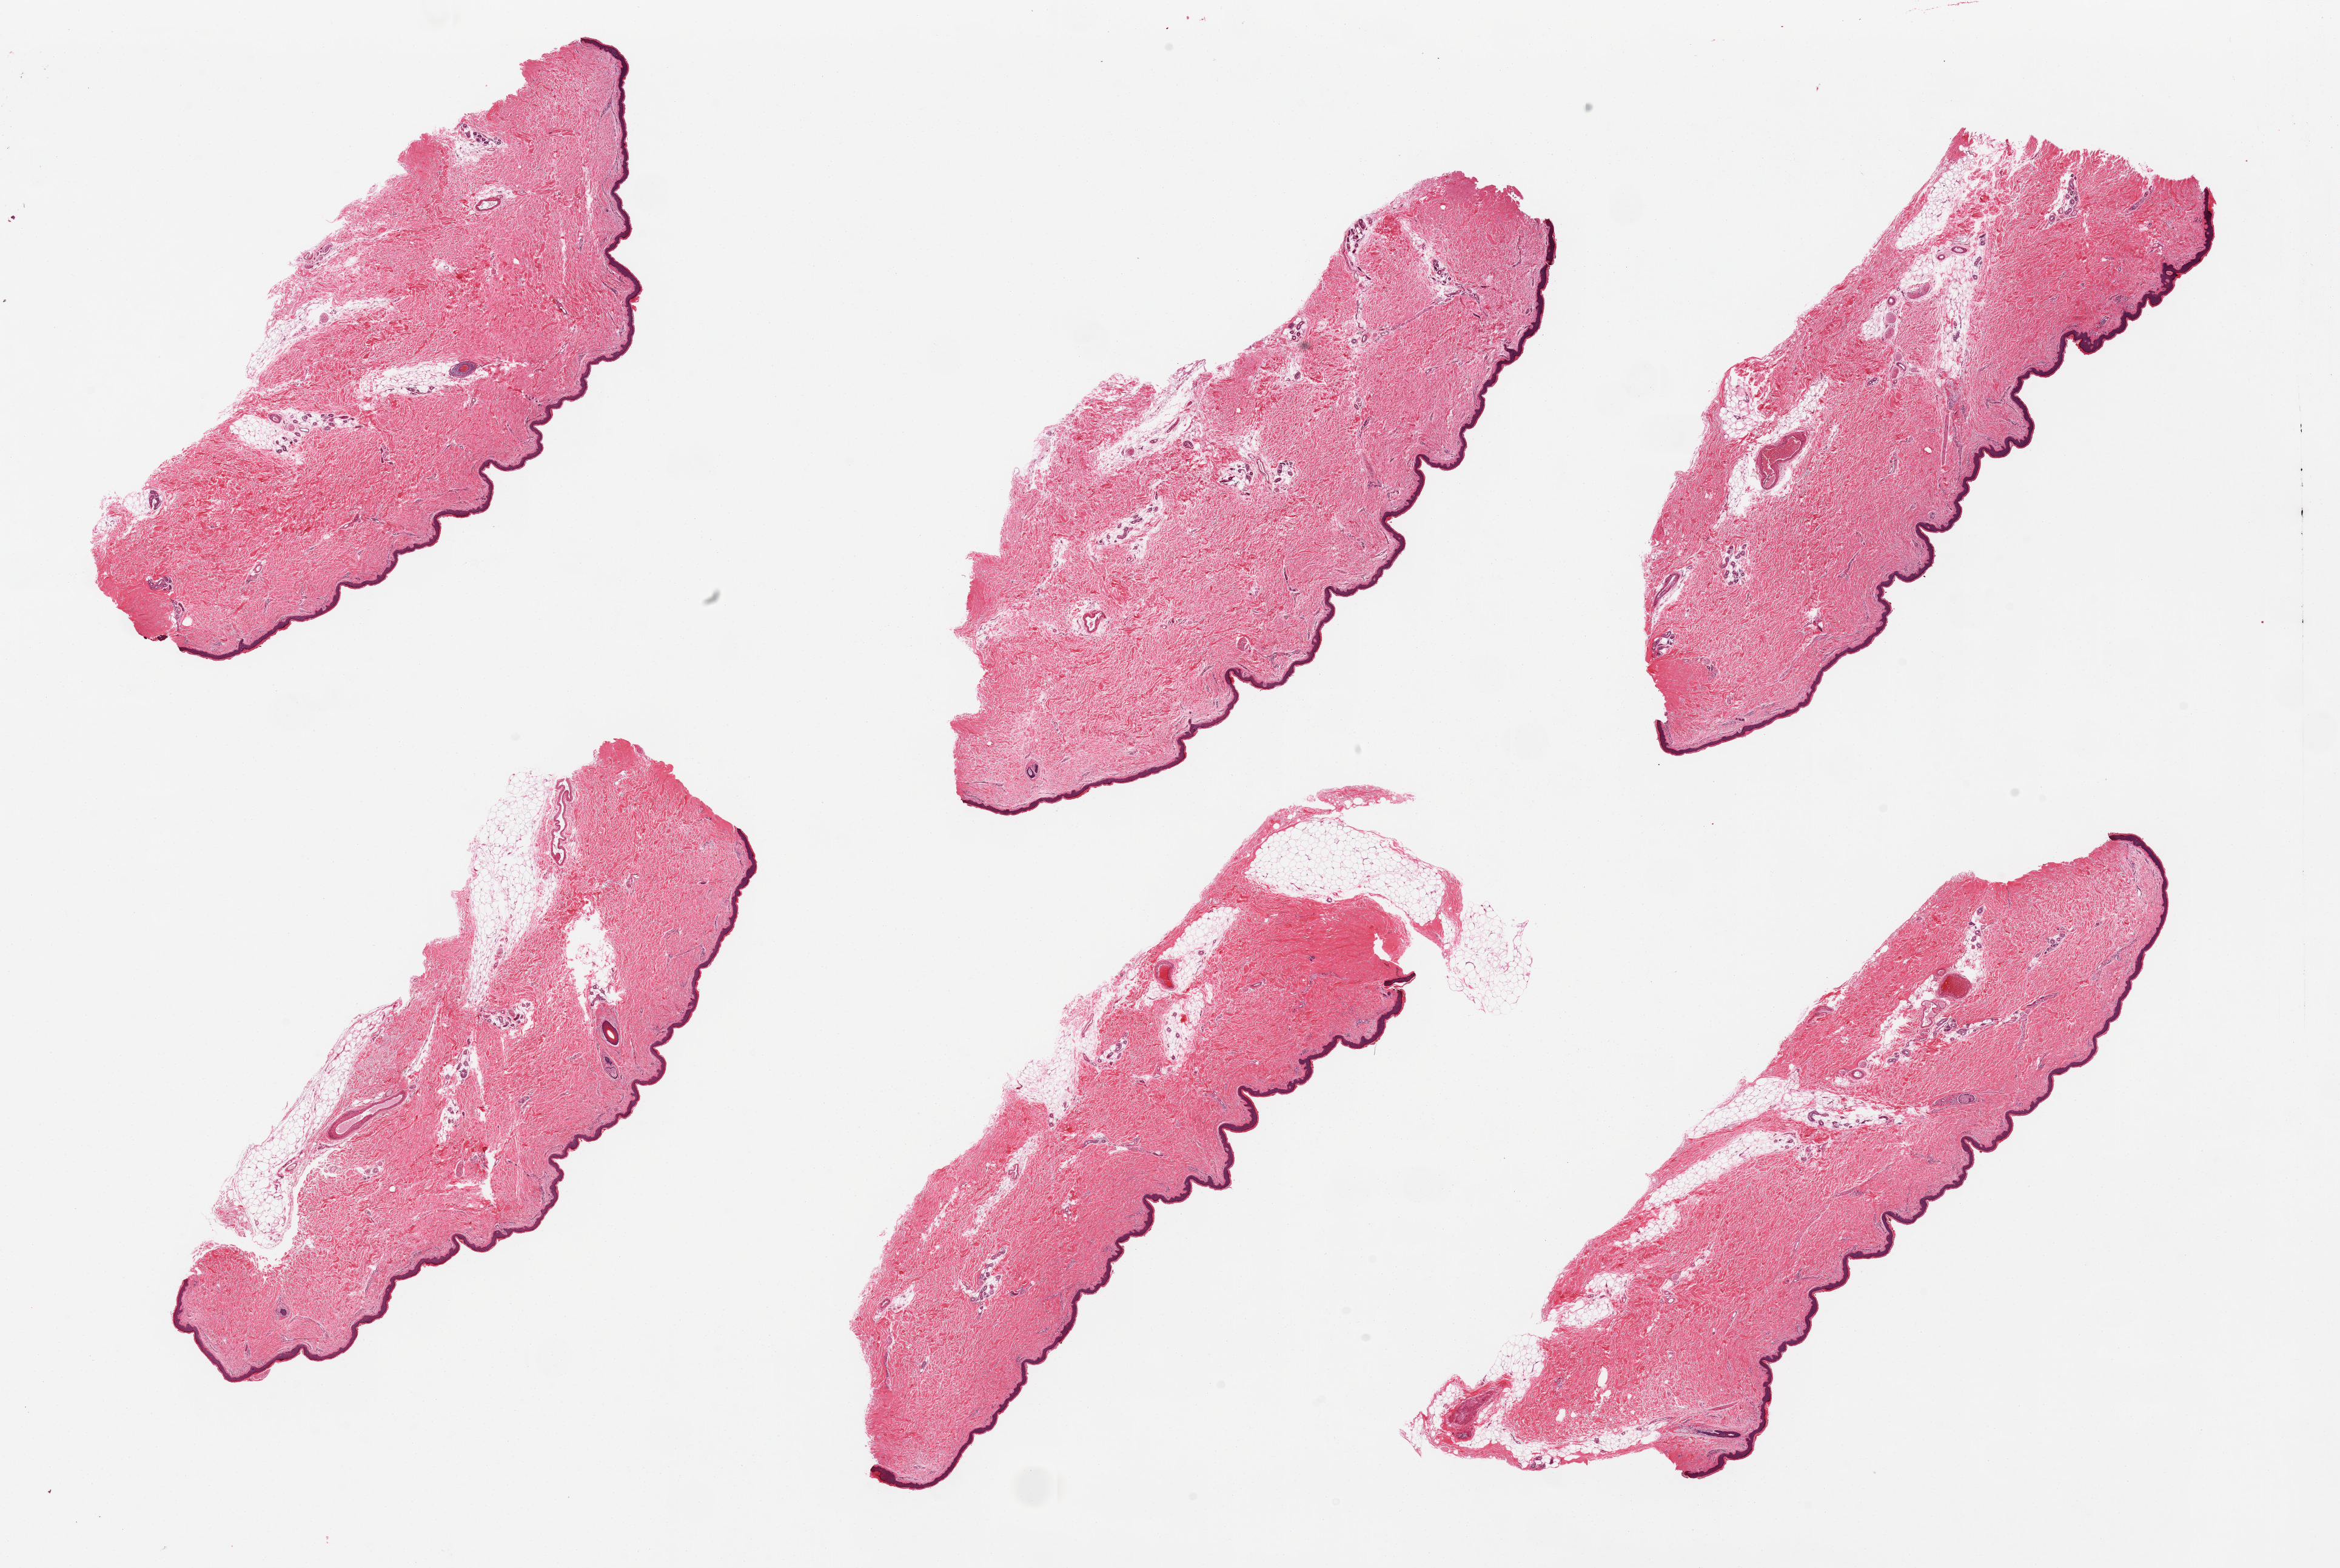
Haematoxylin and eosin whole-slide image — low-resolution overview of the scanned area, about 30.5 x 20.5 mm; PAXgene-fixed, paraffin-embedded tissue; sampled site (target tissue): skin of lower leg; tissue donor sample. Male donor.
- review note (as recorded): 6 pieces, some pieces include up to 10% attached and internal adipose tissue